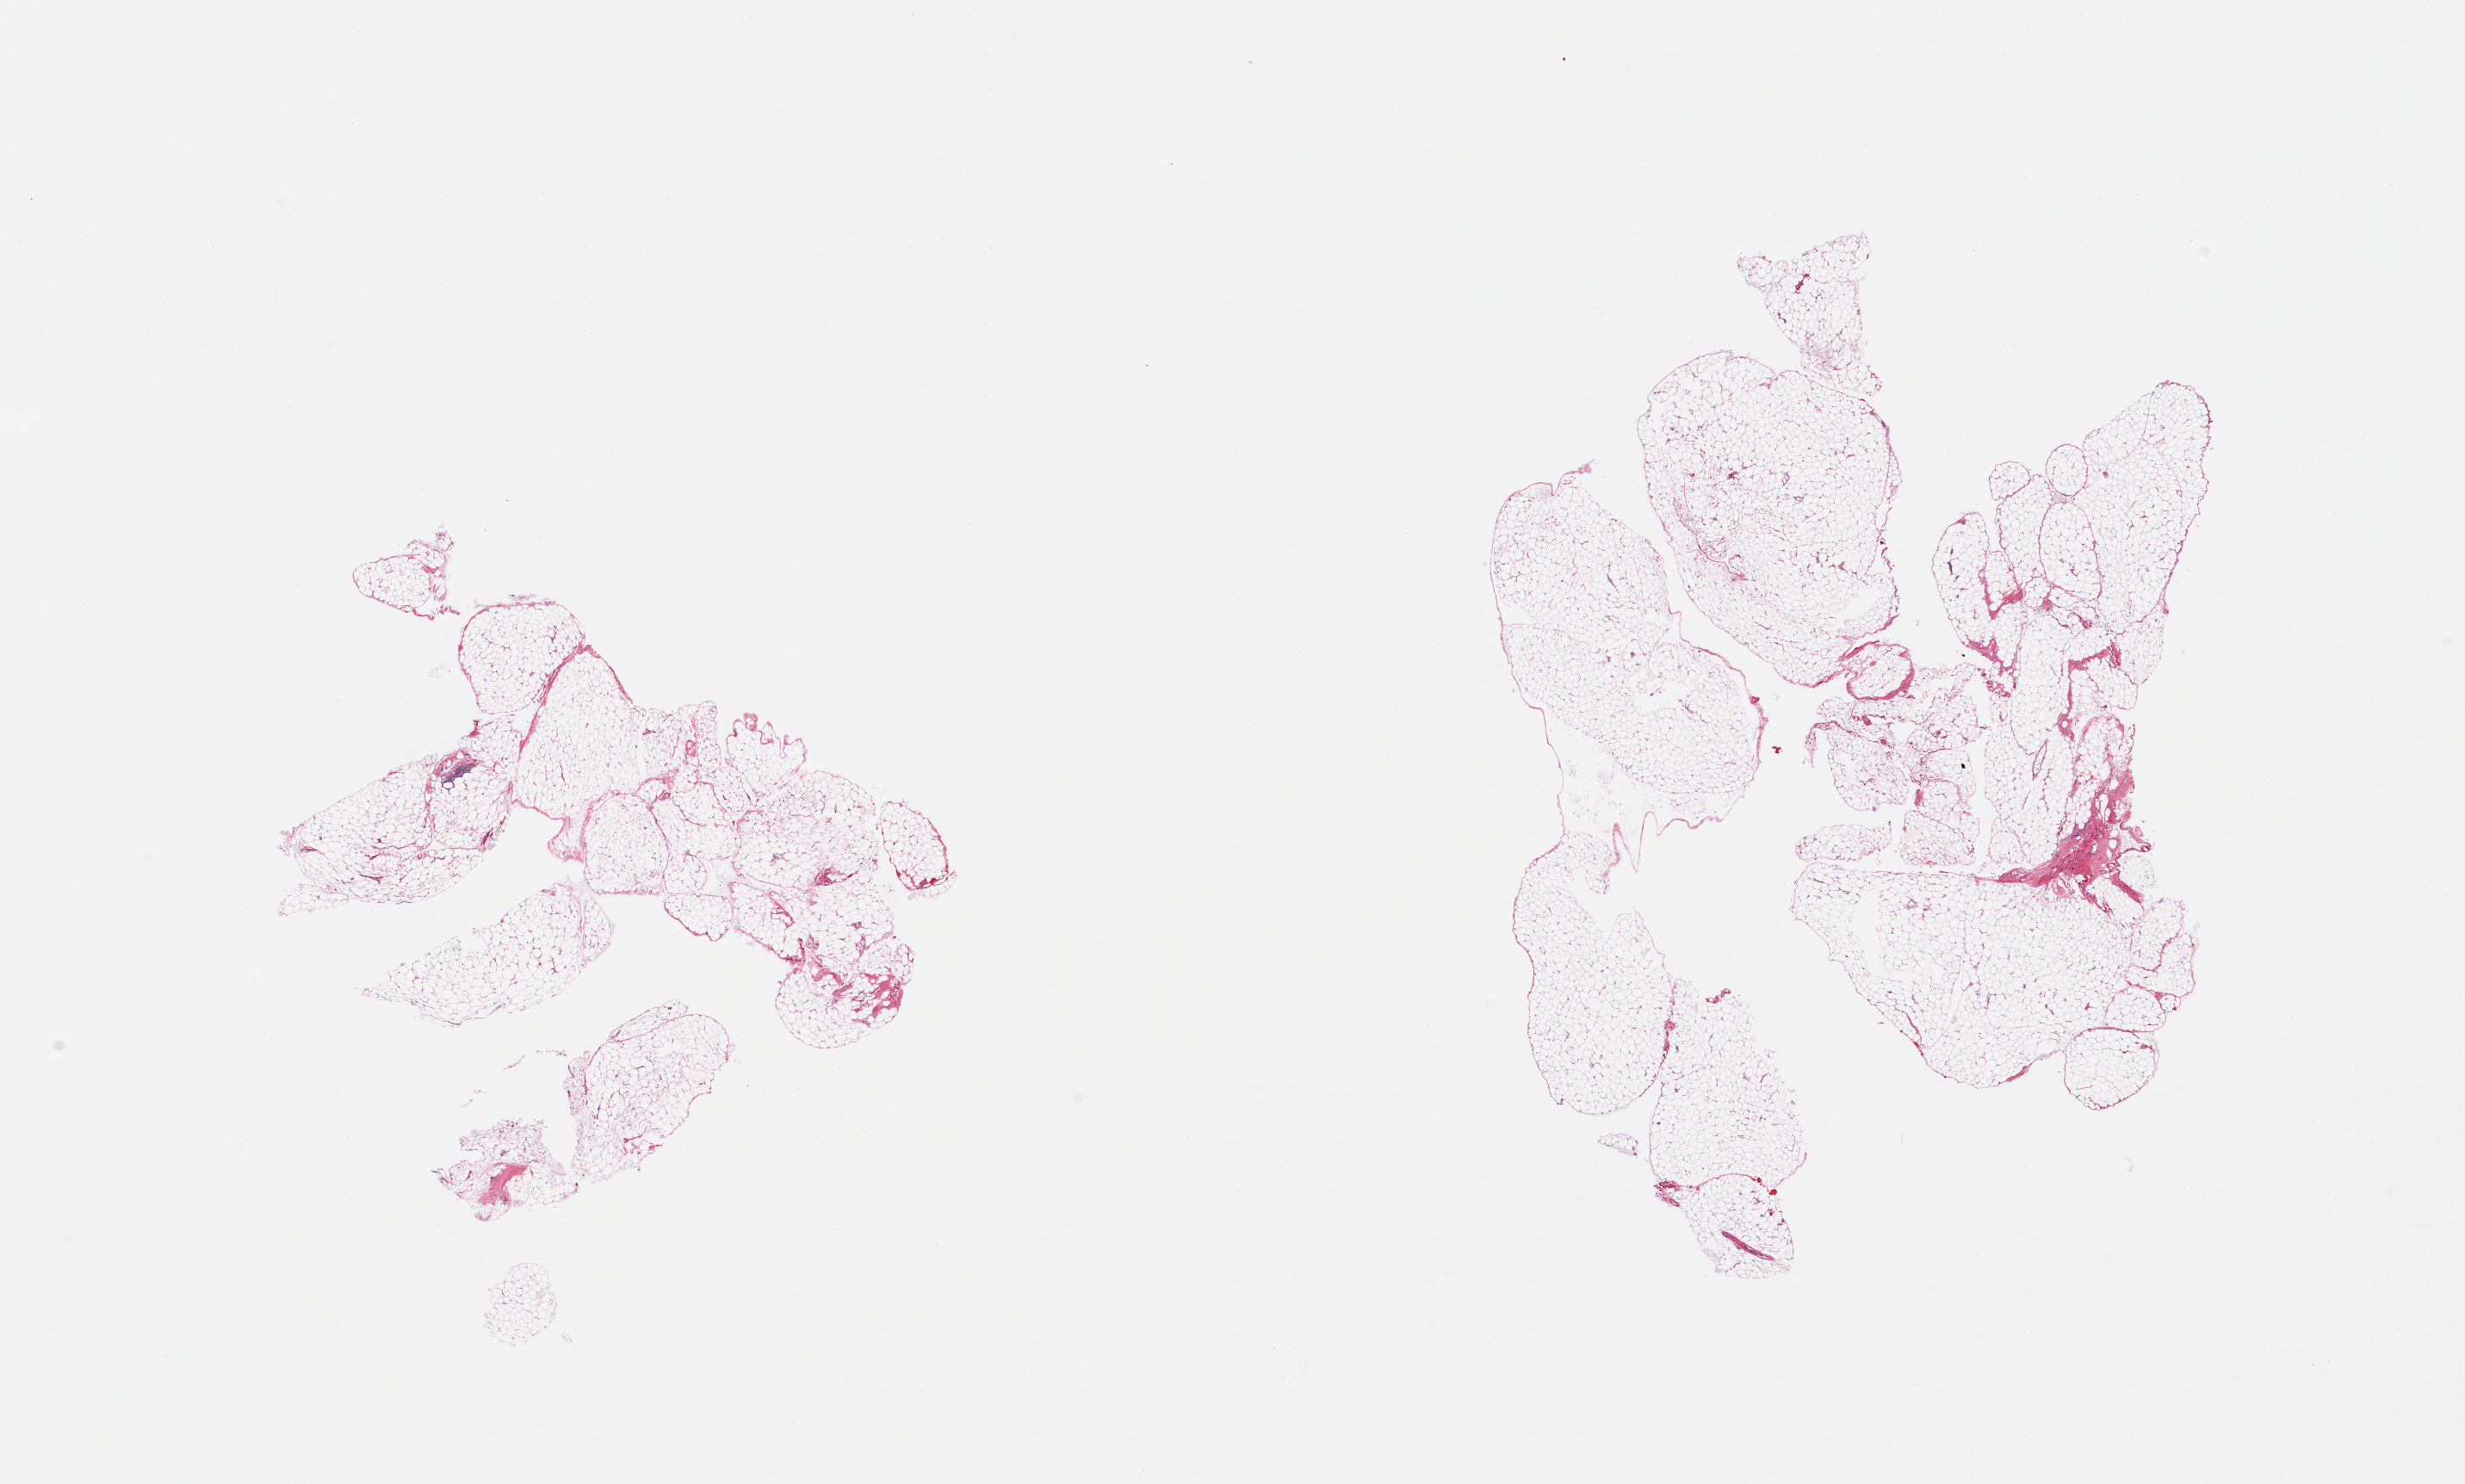
Digitized haematoxylin and eosin-stained section, a low-resolution overview of the entire scanned area, about 22.6 x 13.6 mm (acquisition: 20x scan); PAXgene-fixed paraffin-embedded (PFPE) section; target tissue: omentum; donor tissue sample.
Reviewer comment on this tissue sample: 2 pieces; mature fat, minimal fibrous tissue, focal collection of lymphocytes.